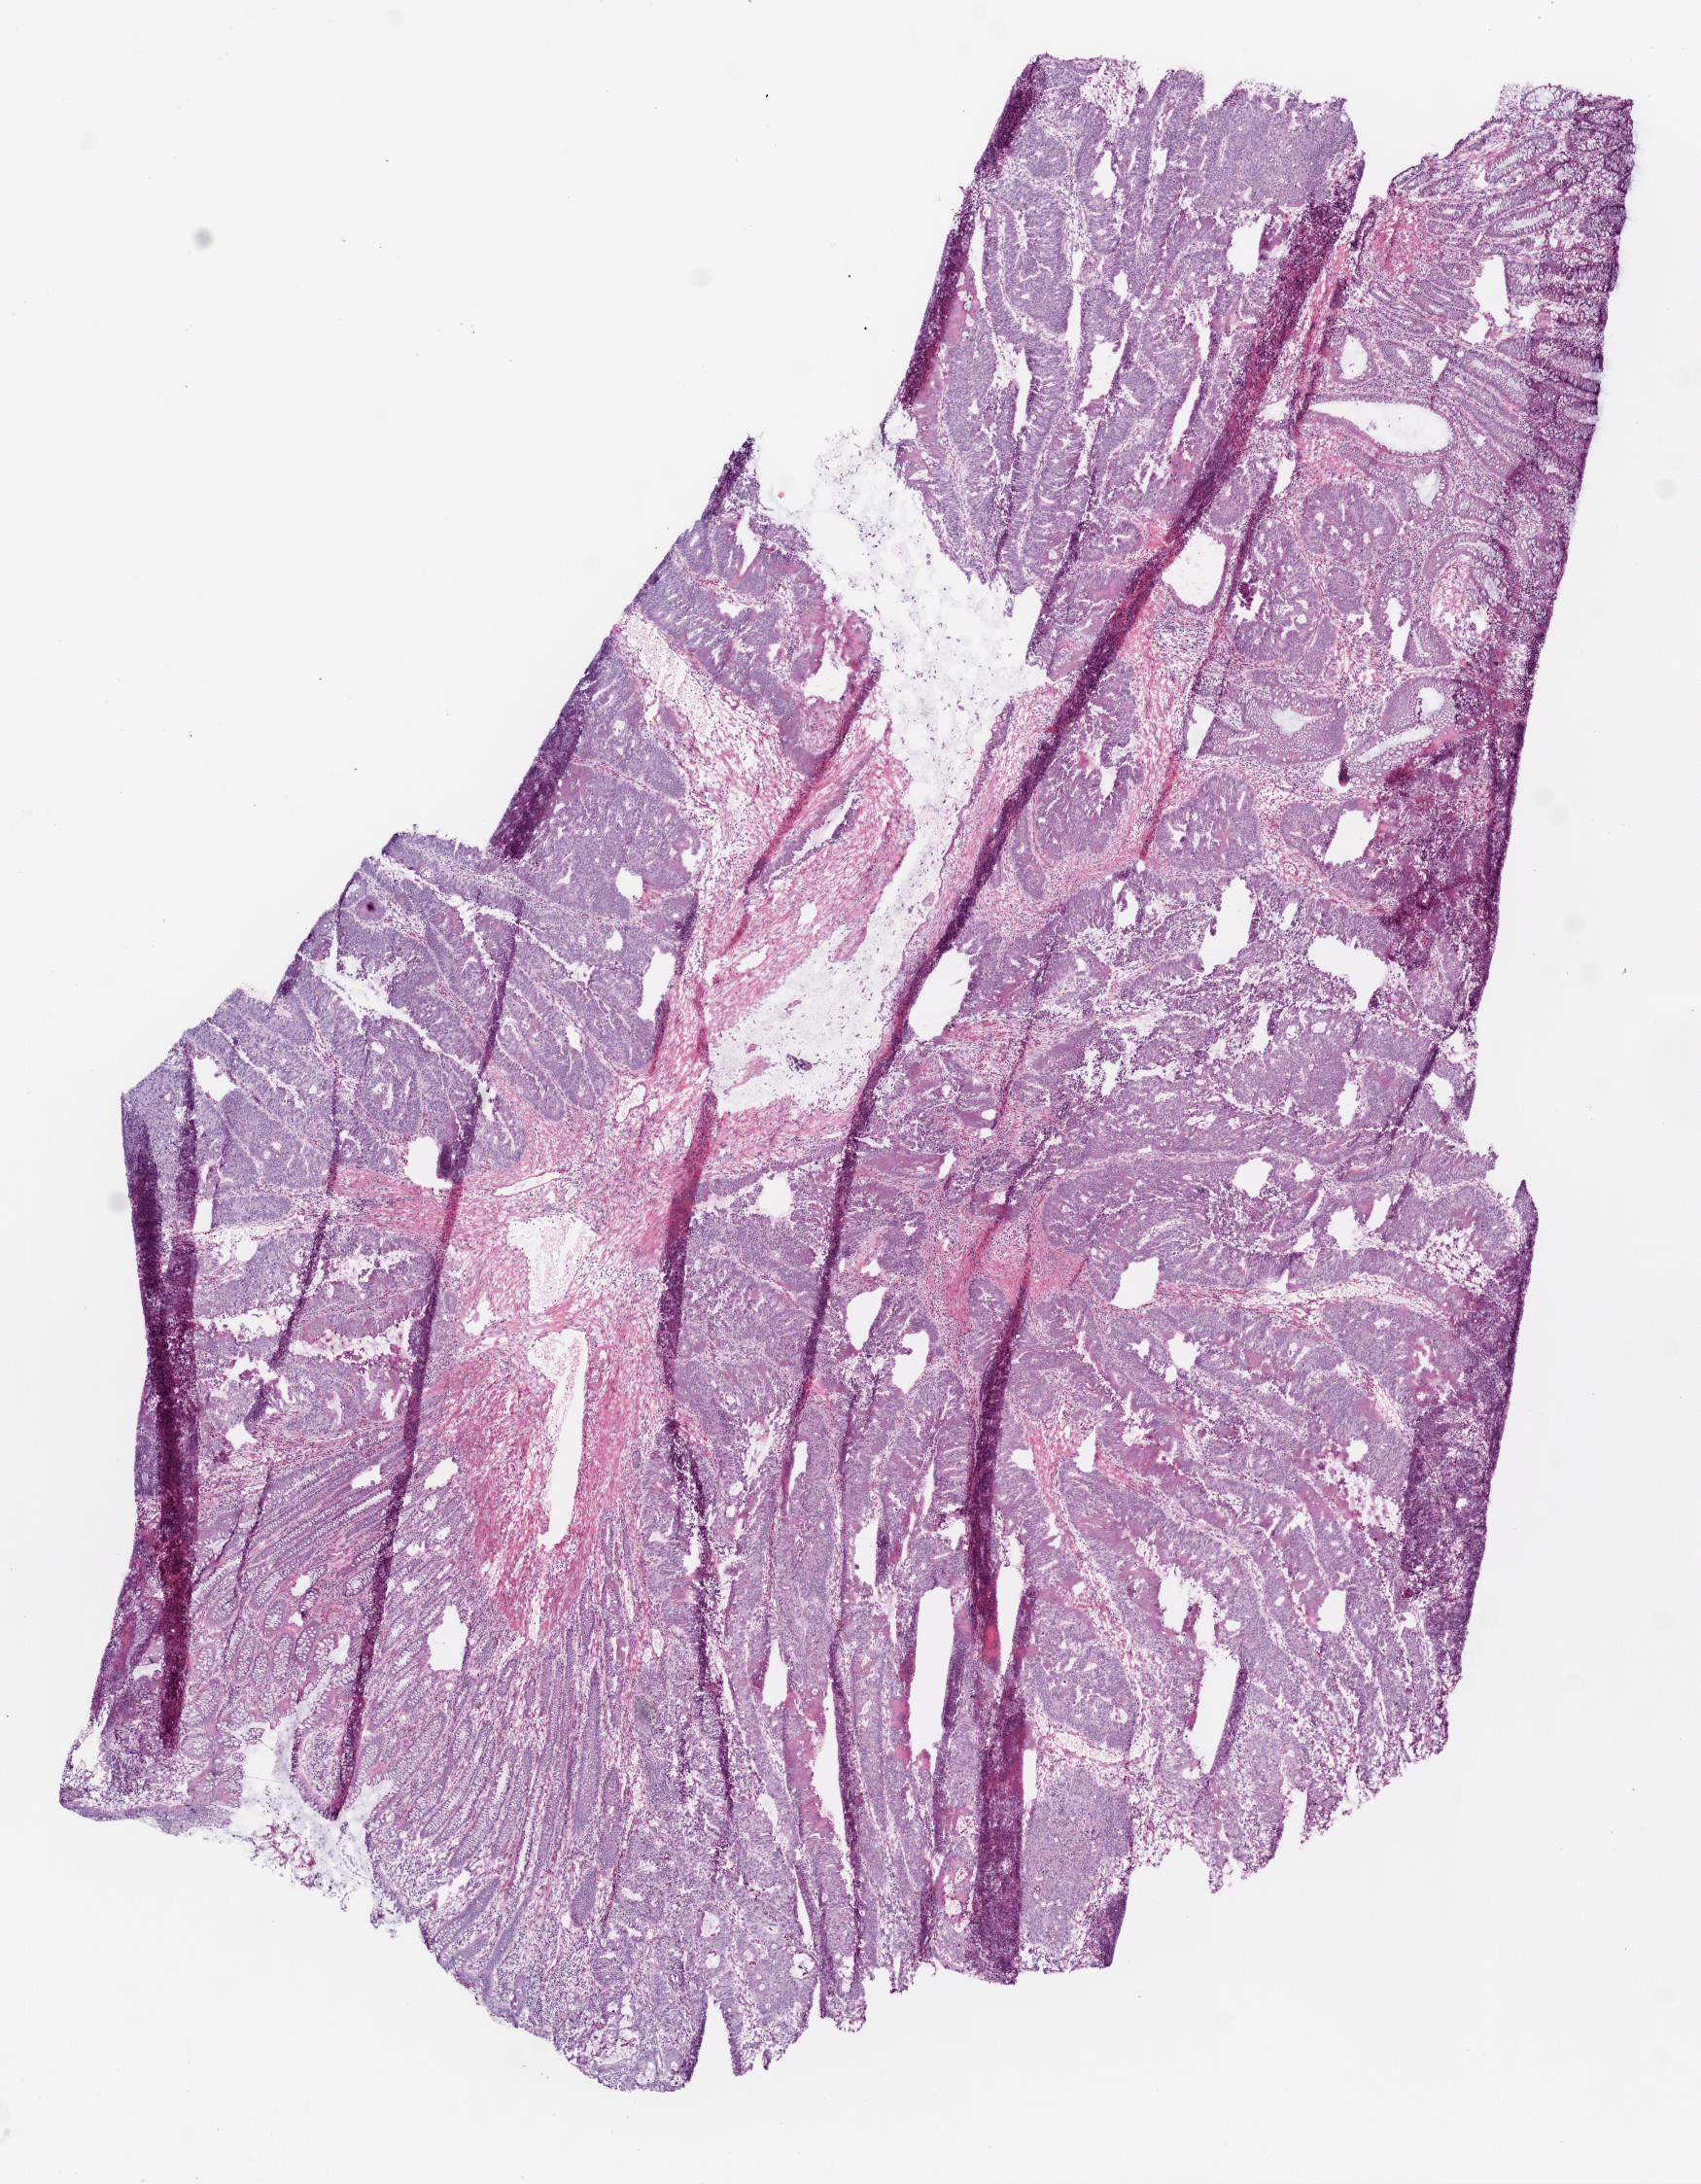
H&E-stained whole-slide image, whole scanned area (about 7.0 x 9.0 mm) shown as a low-resolution overview, frozen section from the bottom of the tissue portion, sample: primary tumour, rectum. Male patient; age at initial diagnosis 66 years. Composition of this section per pathologist review: tumour cells 72%, tumour nuclei 75%.
Diagnosis: Adenocarcinoma, NOS (rectosigmoid junction).